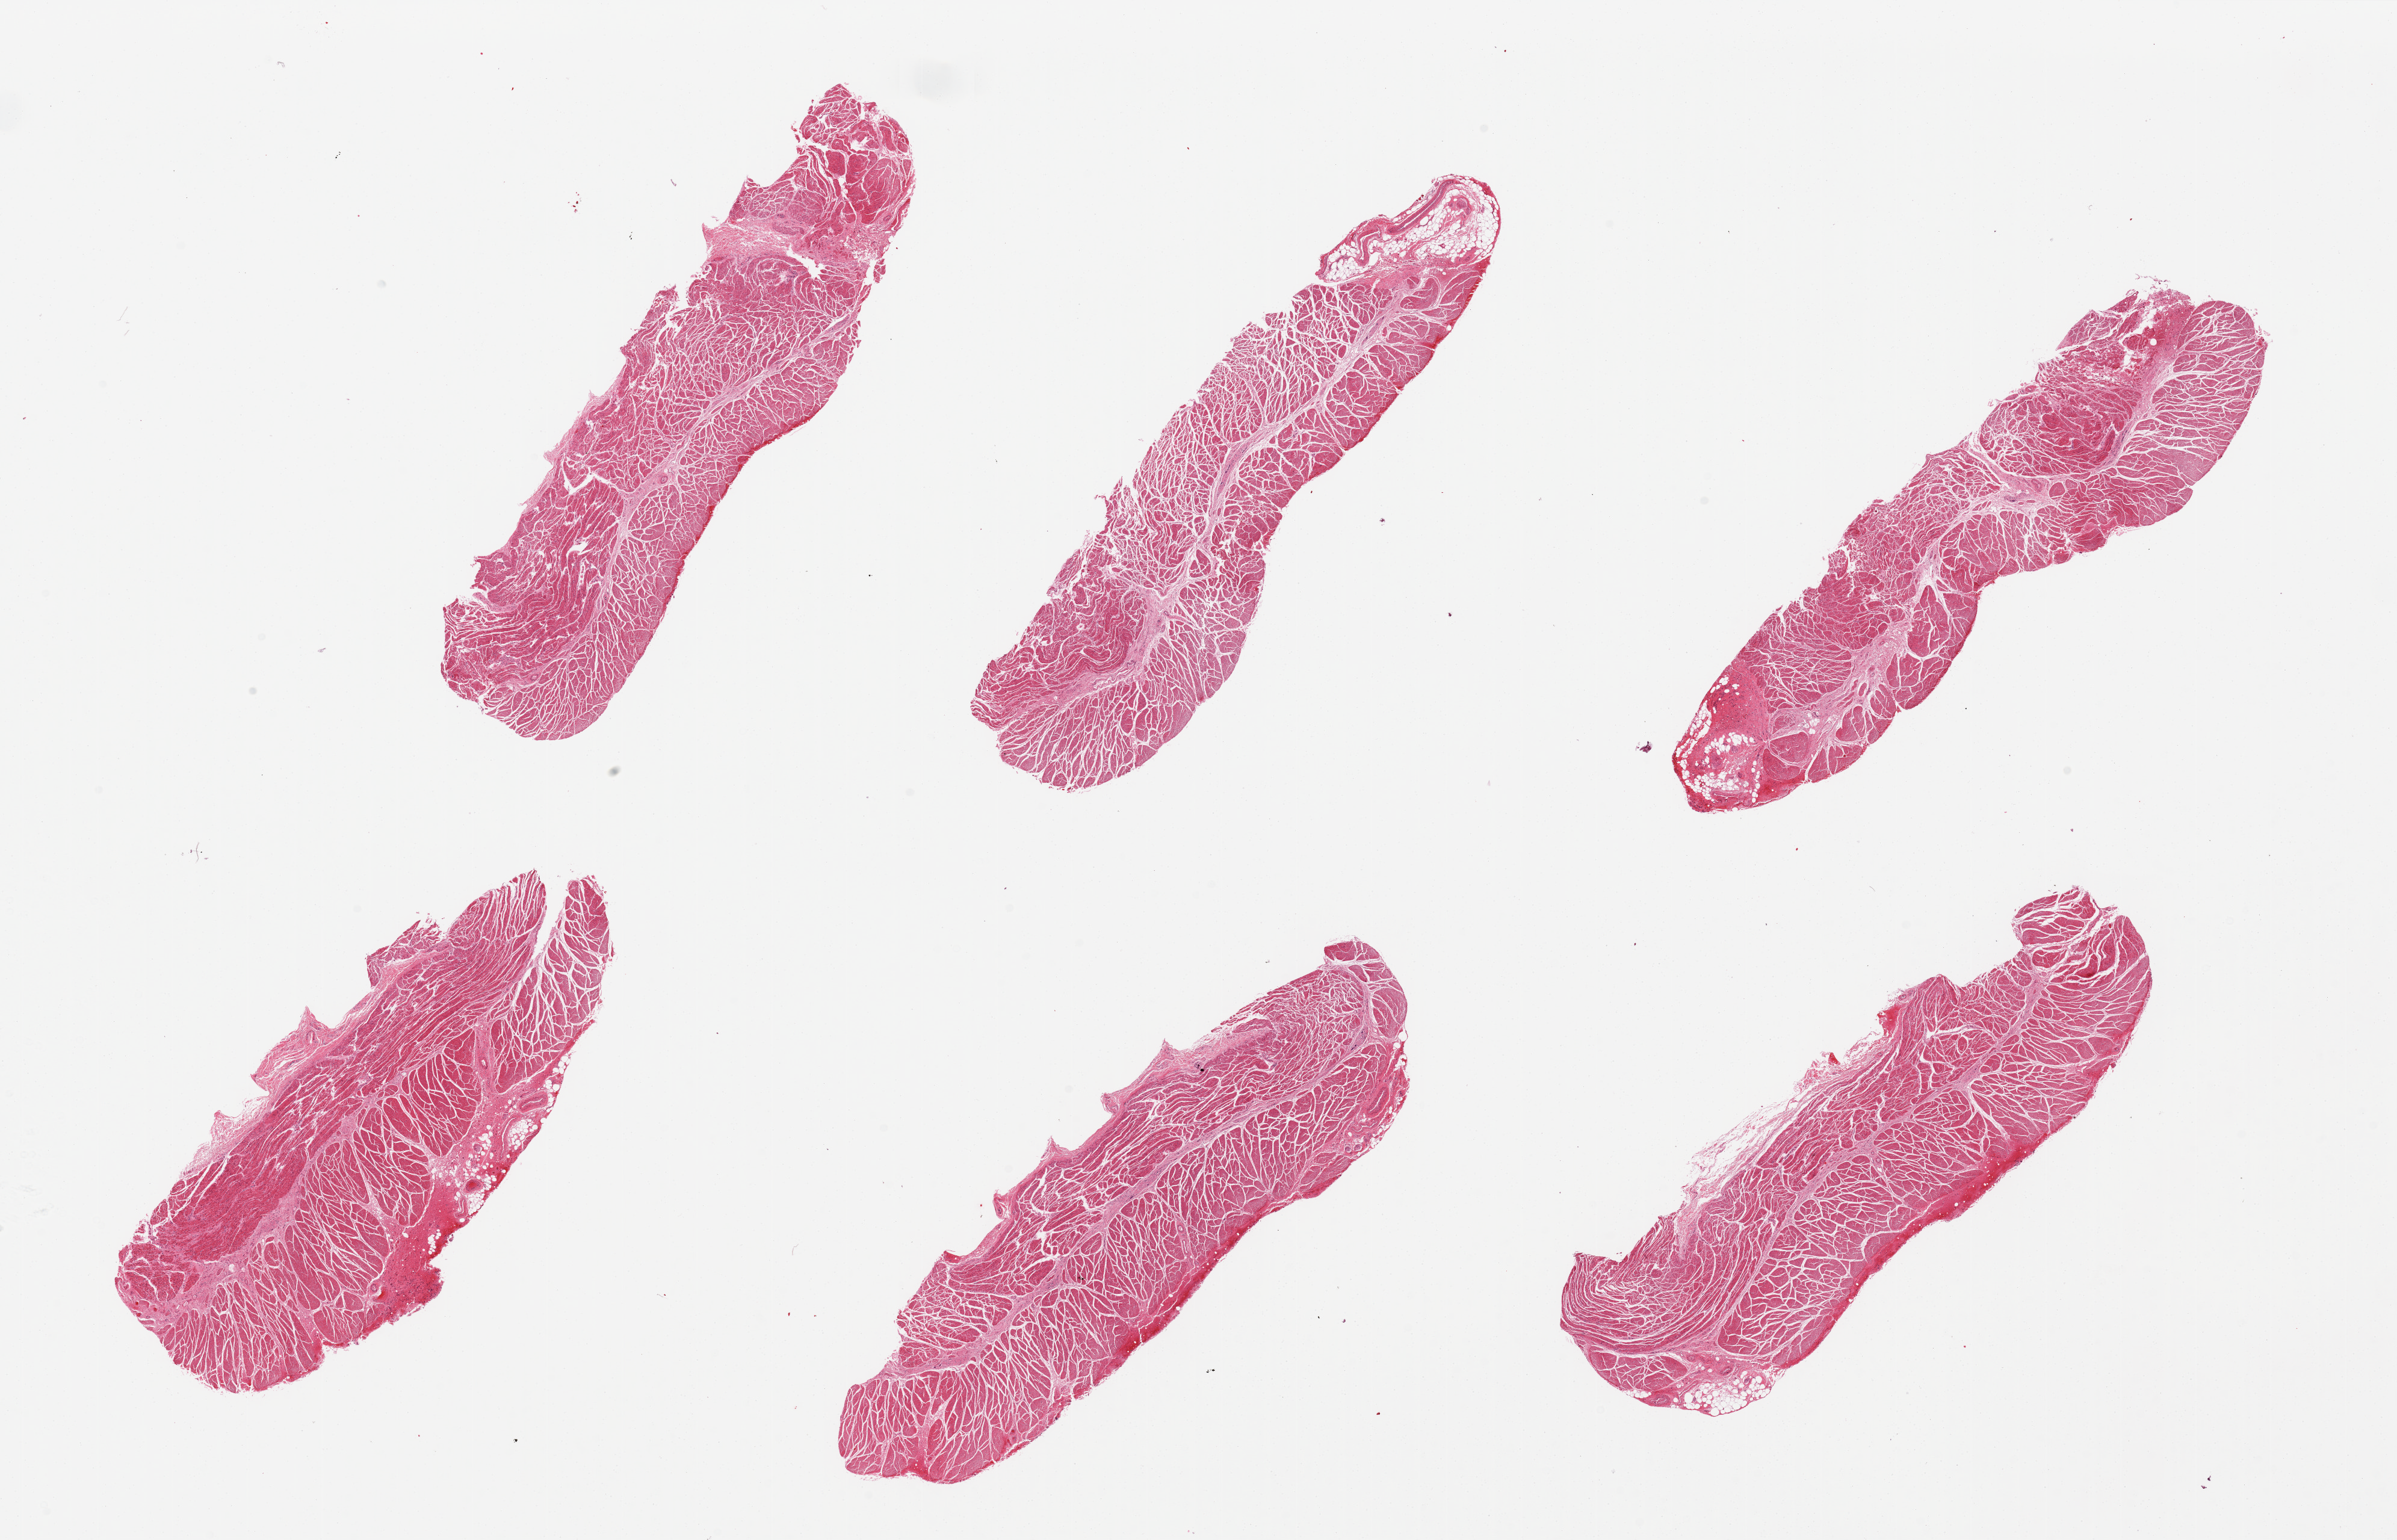
Whole-slide image, haematoxylin and eosin stain — whole scanned area (about 31.5 x 20.2 mm) shown as a low-resolution overview, PAXgene-fixed, paraffin-embedded tissue, sampled site (target tissue): esophageal muscle, tissue donor sample. Donor sex: male.
Review note (as recorded): 6 pieces, well trimmed.